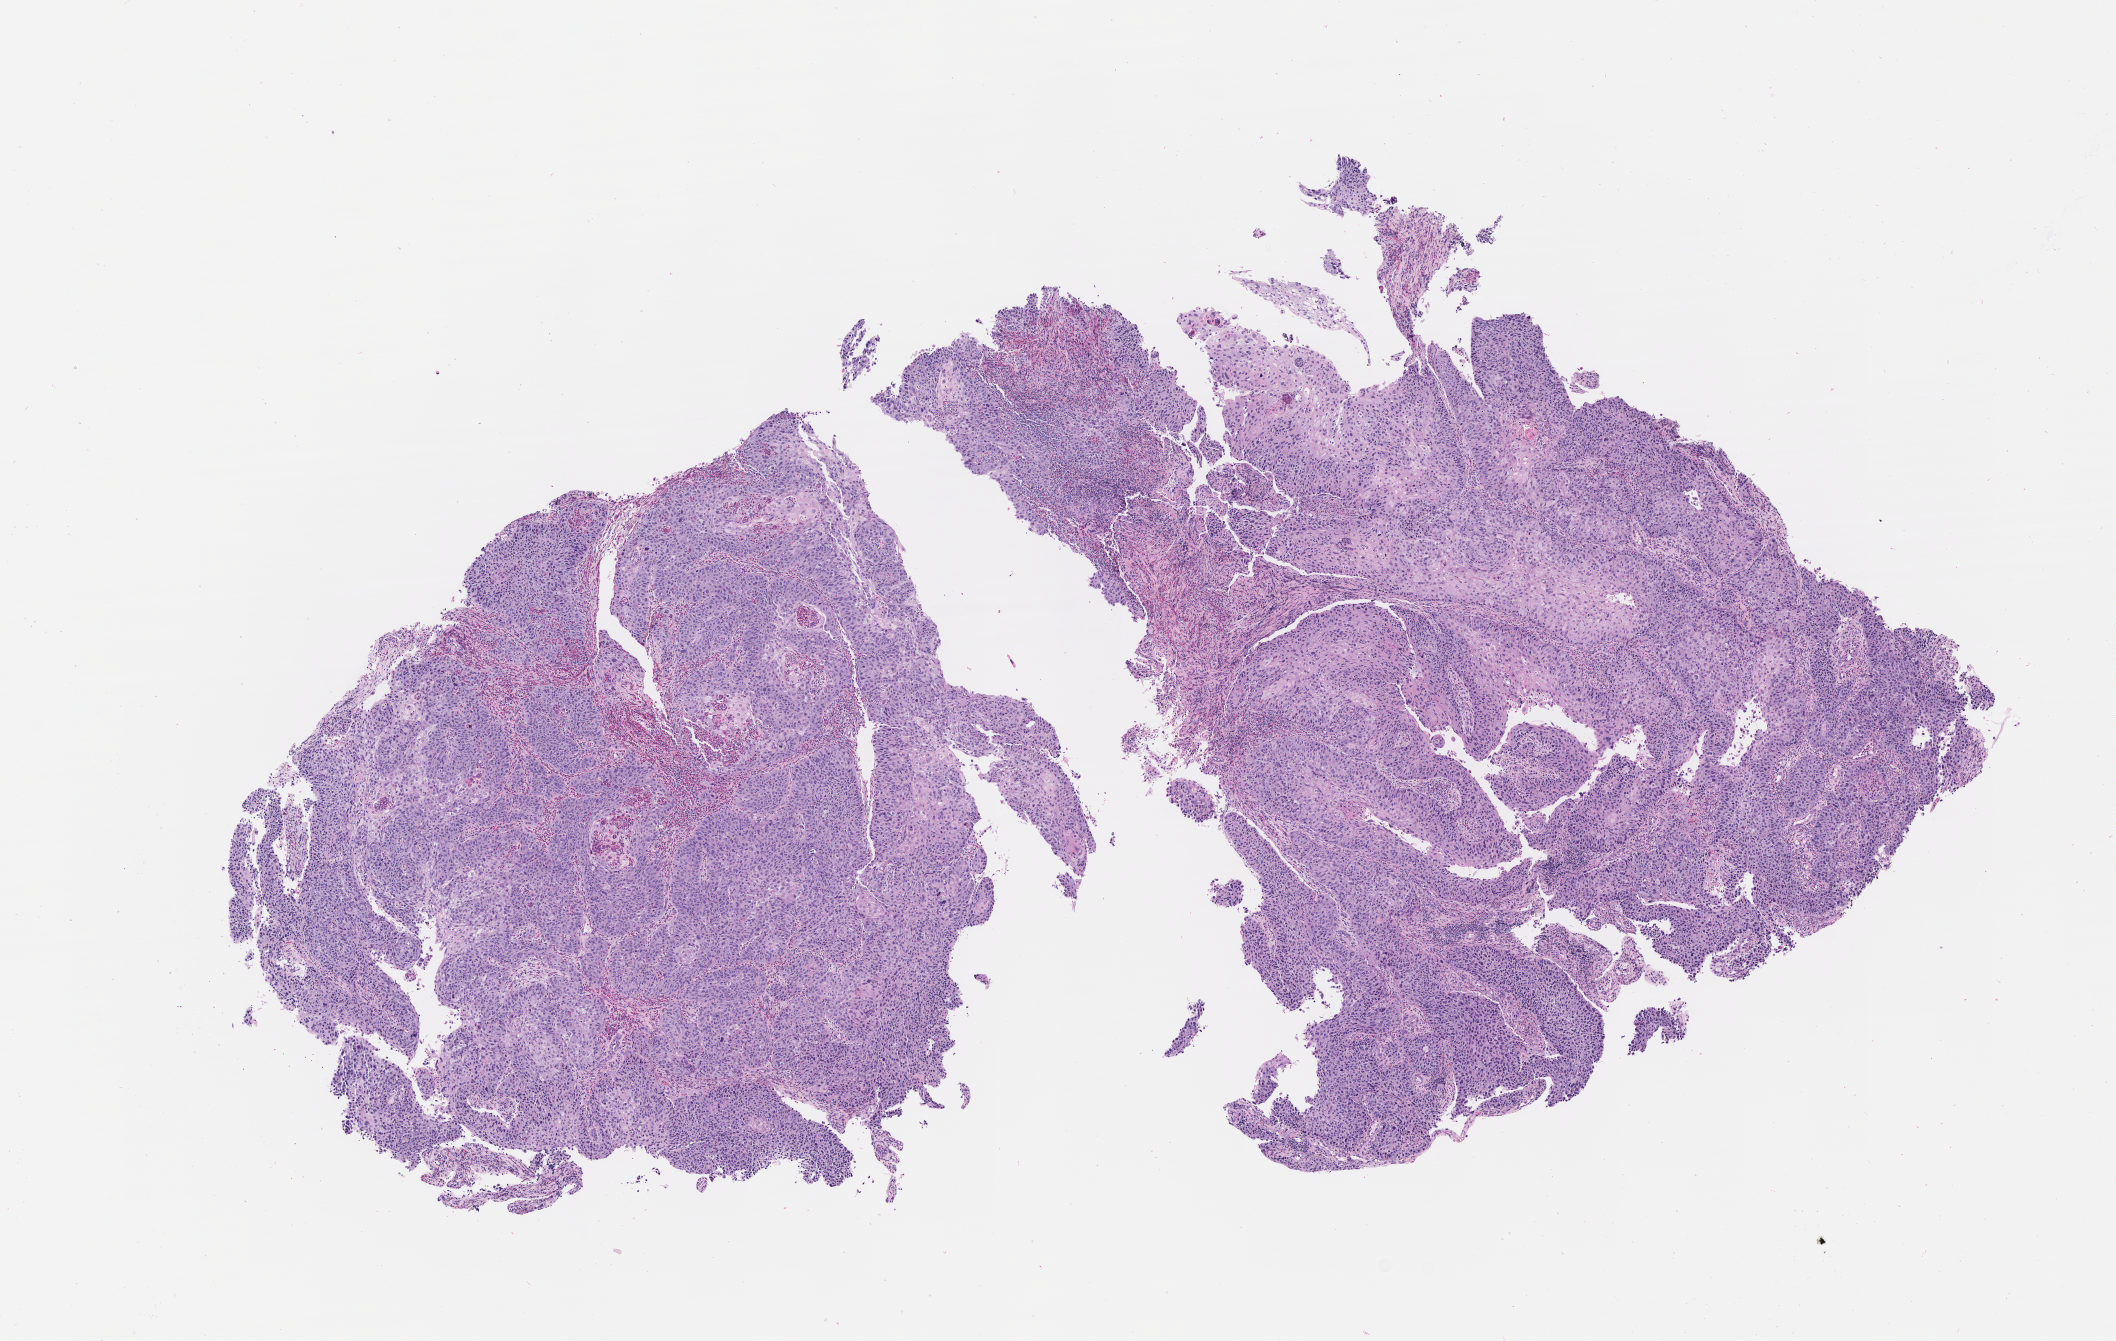
Digitized haematoxylin and eosin-stained section — shown as a low-resolution overview of the whole scanned area (about 8.6 x 5.4 mm), tumor tissue, anatomic site: cervix. Female patient, aged 33.
Histologic diagnosis: Squamous cell carcinoma, large cell, nonkeratinizing, NOS.